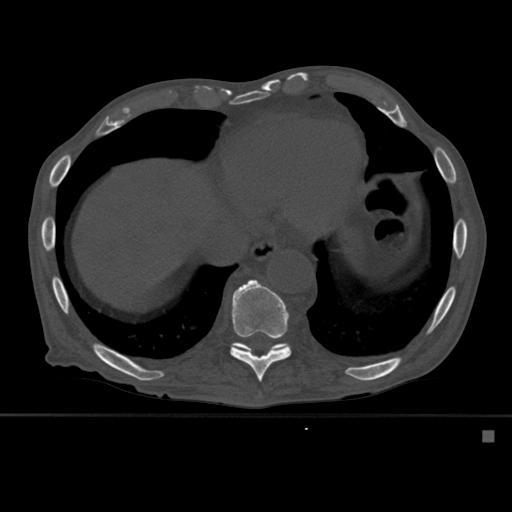
CT including the spine, one axial slice. Position 312 of 527 along the scan axis. Bone window (W 1800 / L 400 HU). 512 × 512 image matrix, field of view 373 × 373 mm. Patient: male, 78 years. Case-level facts recorded for this patient, not image findings: primary cancer: prostate.
Outlined on this slice (semi-automatically segmented with operator editing):
- T10 vertebra: bounding box <230,279,291,382> (left, top, right, bottom; pixels)
- T11 vertebra: <234,337,291,355>